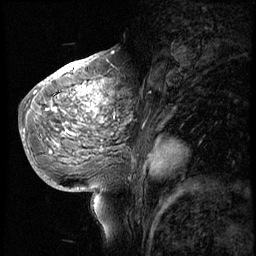
Breast MRI (dynamic contrast-enhanced), one sagittal slice. Slice 30 of 56 in the series (ordered by position). 4 images stored at this slice position (order not interpretable as contrast timing). 1.5 T. TE 4.2 ms, TR 8.9 ms. 2.5 mm slice thickness. 256 × 256 image matrix. Female patient, age 51 years. From the clinical record (not read from this slice): setting: breast cancer imaged before/during neoadjuvant chemotherapy; receptor status: triple-negative.
Annotated regions visible in this slice (semi-automatic segmentation, software-assisted and operator-edited):
- analysis volume of interest (the breast-tissue region the enhancement analysis was run in; not a lesion): bounding box <30,70,150,173> (left, top, right, bottom; pixels)
- tumour enhancement mask (voxels above the 140 % enhancement threshold inside the analysis volume of interest): <36,70,111,135>